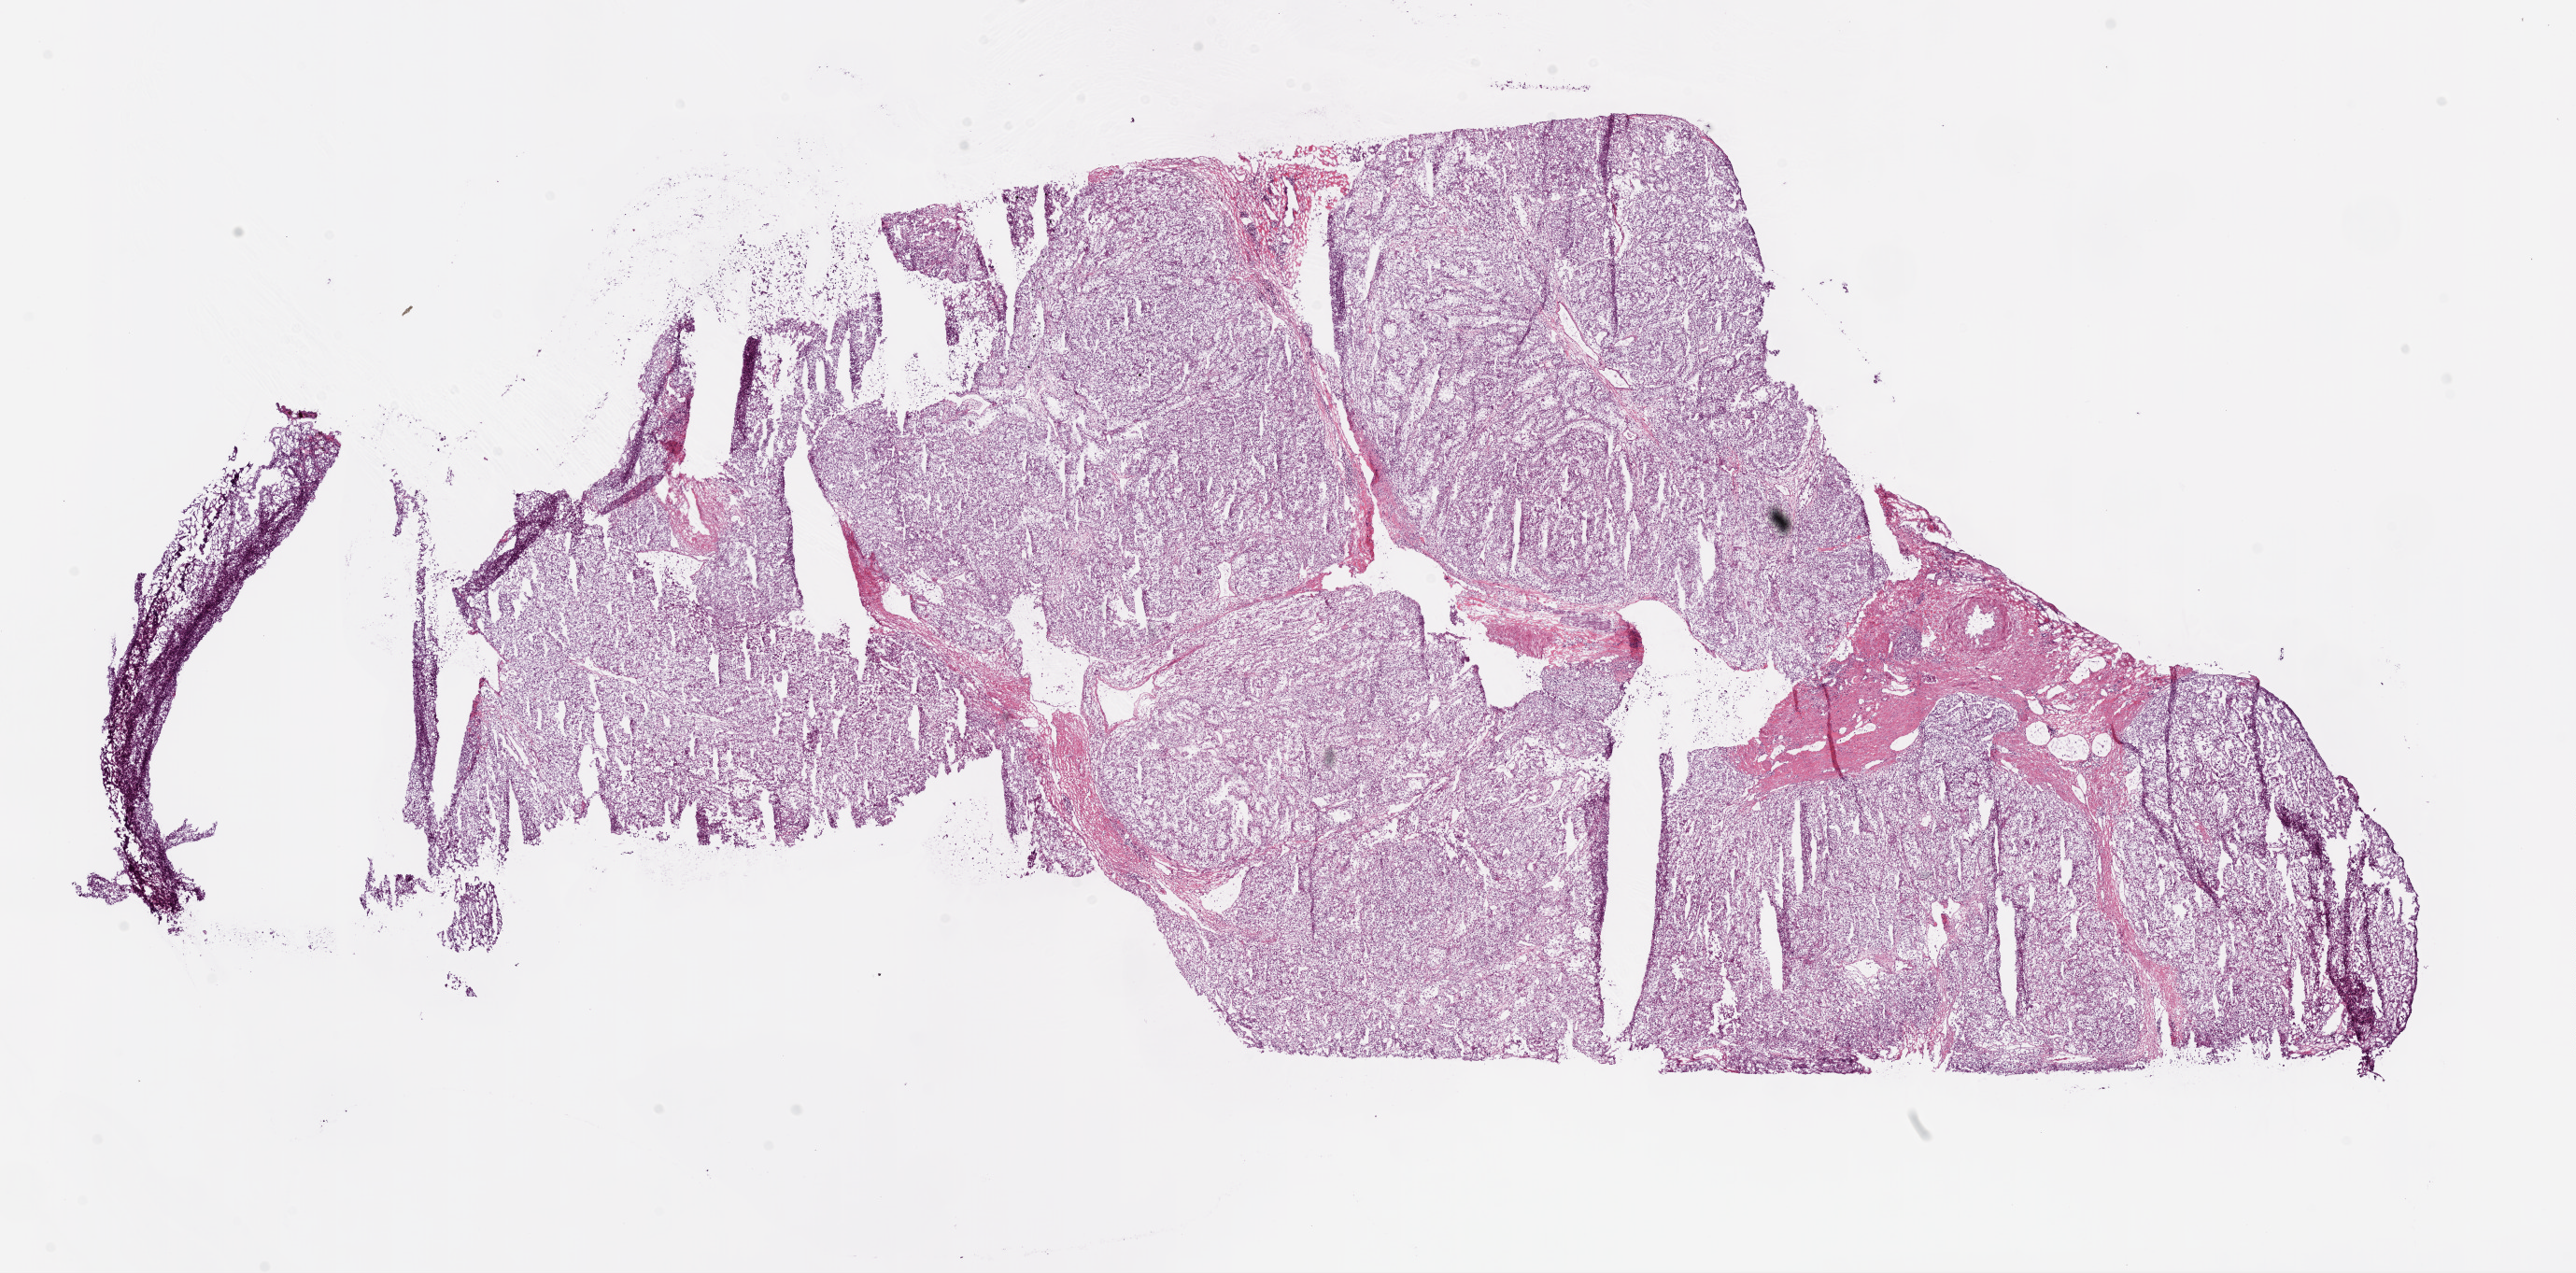
Digitized Hematoxylin and eosin (H&E) stained tissue section (whole slide) — low-resolution overview of the scanned area, about 22.2 x 11.0 mm (acquisition: 20x scan). Frozen section from the bottom of the tissue portion. Kidney, primary tumour sample. Male patient; age at initial diagnosis 60 years. Histologic grade: G4 (undifferentiated). Pathologist review of this section (percent, as recorded): tumour cells 88%, tumour nuclei 85%, normal cells 0%, stromal cells 12%, necrosis 0%.
Histologic diagnosis: Clear cell adenocarcinoma, NOS. AJCC pathologic stage: IV (7th edition).